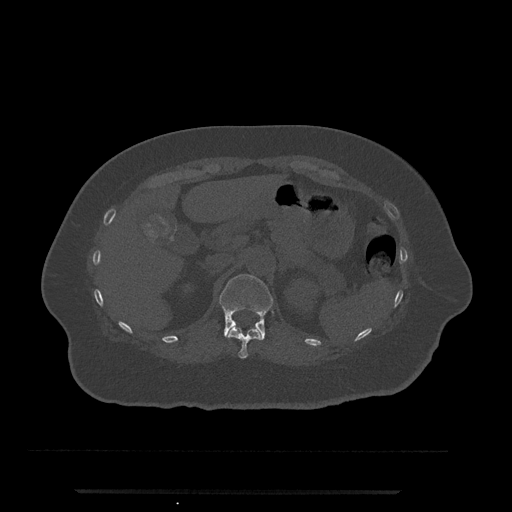
CT including the spine, one axial slice. Slice 195 of 797 in the series (ordered by position). Reconstruction kernel Br40s/3. Bone window (W 1800 / L 400 HU). 0.5 mm slice thickness. 512 × 512 image matrix. Patient: female, 51 years. Case-level facts recorded for this patient, not image findings: primary cancer: neuro; vertebrae with lytic lesions (as recorded): T8.
Structures marked on this image (semi-automatic segmentation, software-assisted and operator-edited):
- T11 vertebra: bounding box [x1, y1, x2, y2] px = [226, 327, 261, 359]
- T12 vertebra: [219, 274, 274, 341]